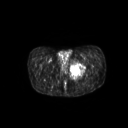
FDG PET of an extremity soft-tissue mass (from a PET/CT study), one axial slice. Position 40 of 267 along the scan axis. 3.27 mm slice thickness. 128 × 128 image matrix, field of view 600 × 600 mm. Male patient, age 59 years. From the clinical record (not read from this slice): histological type: pleiomorphic liposarcoma; grade: high; site of the primary tumour: left thigh.
Outlined on this slice (expert contour drawn on MRI and transferred to this co-registered scan by the dataset authors):
- gross tumour volume including surrounding oedema: bounding box <70,62,85,79> (left, top, right, bottom; pixels)
- gross tumour volume (mass): <70,63,84,75>